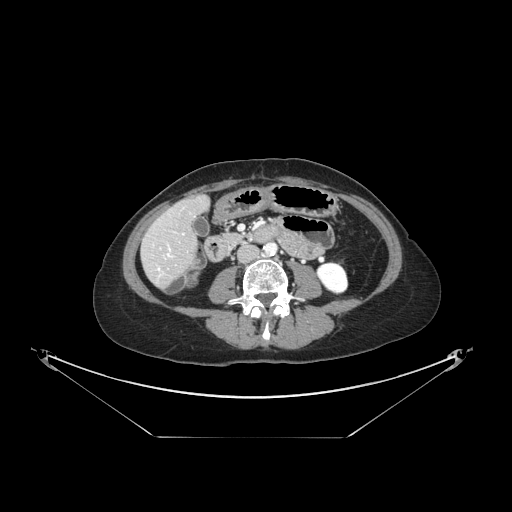
Contrast-enhanced abdominal CT, one axial slice. Position 39 of 148 along the scan axis. 120 kVp. Soft-tissue window (W 400 / L 40 HU). 512 × 512 image matrix, field of view 500 × 500 mm. Female patient, age 73 years. Case-level facts recorded for this patient, not image findings: diagnosis: colorectal cancer liver metastases, imaged before liver resection; multiple liver metastases: no; largest metastasis: 1 cm.
Structures marked on this image (manually delineated by an expert):
- hepatic veins: bounding box (x1, y1, x2, y2) in pixels: (158, 253, 172, 272)
- liver: (143, 197, 208, 286)
- planned liver remnant (the part of the liver to remain after resection): (161, 197, 207, 240)